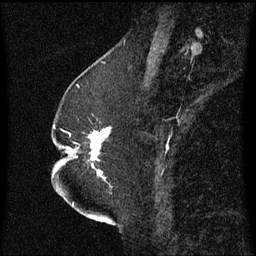
Breast MRI (dynamic contrast-enhanced), one sagittal slice. Slice 23 of 60 in the series (ordered by position). Dynamic contrast-enhanced series, image 2 of 3 at this slice position (ordered by acquisition). 1.5 T. TE 4.2 ms, TR 8.4 ms. 2.3 mm slice thickness. 256 × 256 image matrix, field of view 200 × 200 mm. Patient: female, 52 years. From the clinical record (not read from this slice): setting: breast cancer imaged before/during neoadjuvant chemotherapy; receptor status: HR-positive, HER2-negative.
Structures marked on this image (semi-automatic segmentation, software-assisted and operator-edited):
- analysis volume of interest (the breast-tissue region the enhancement analysis was run in; not a lesion): bounding box (x1, y1, x2, y2) in pixels: (65, 128, 113, 183)
- tumour enhancement mask (voxels above the 70 % enhancement threshold inside the analysis volume of interest): (90, 128, 112, 177)